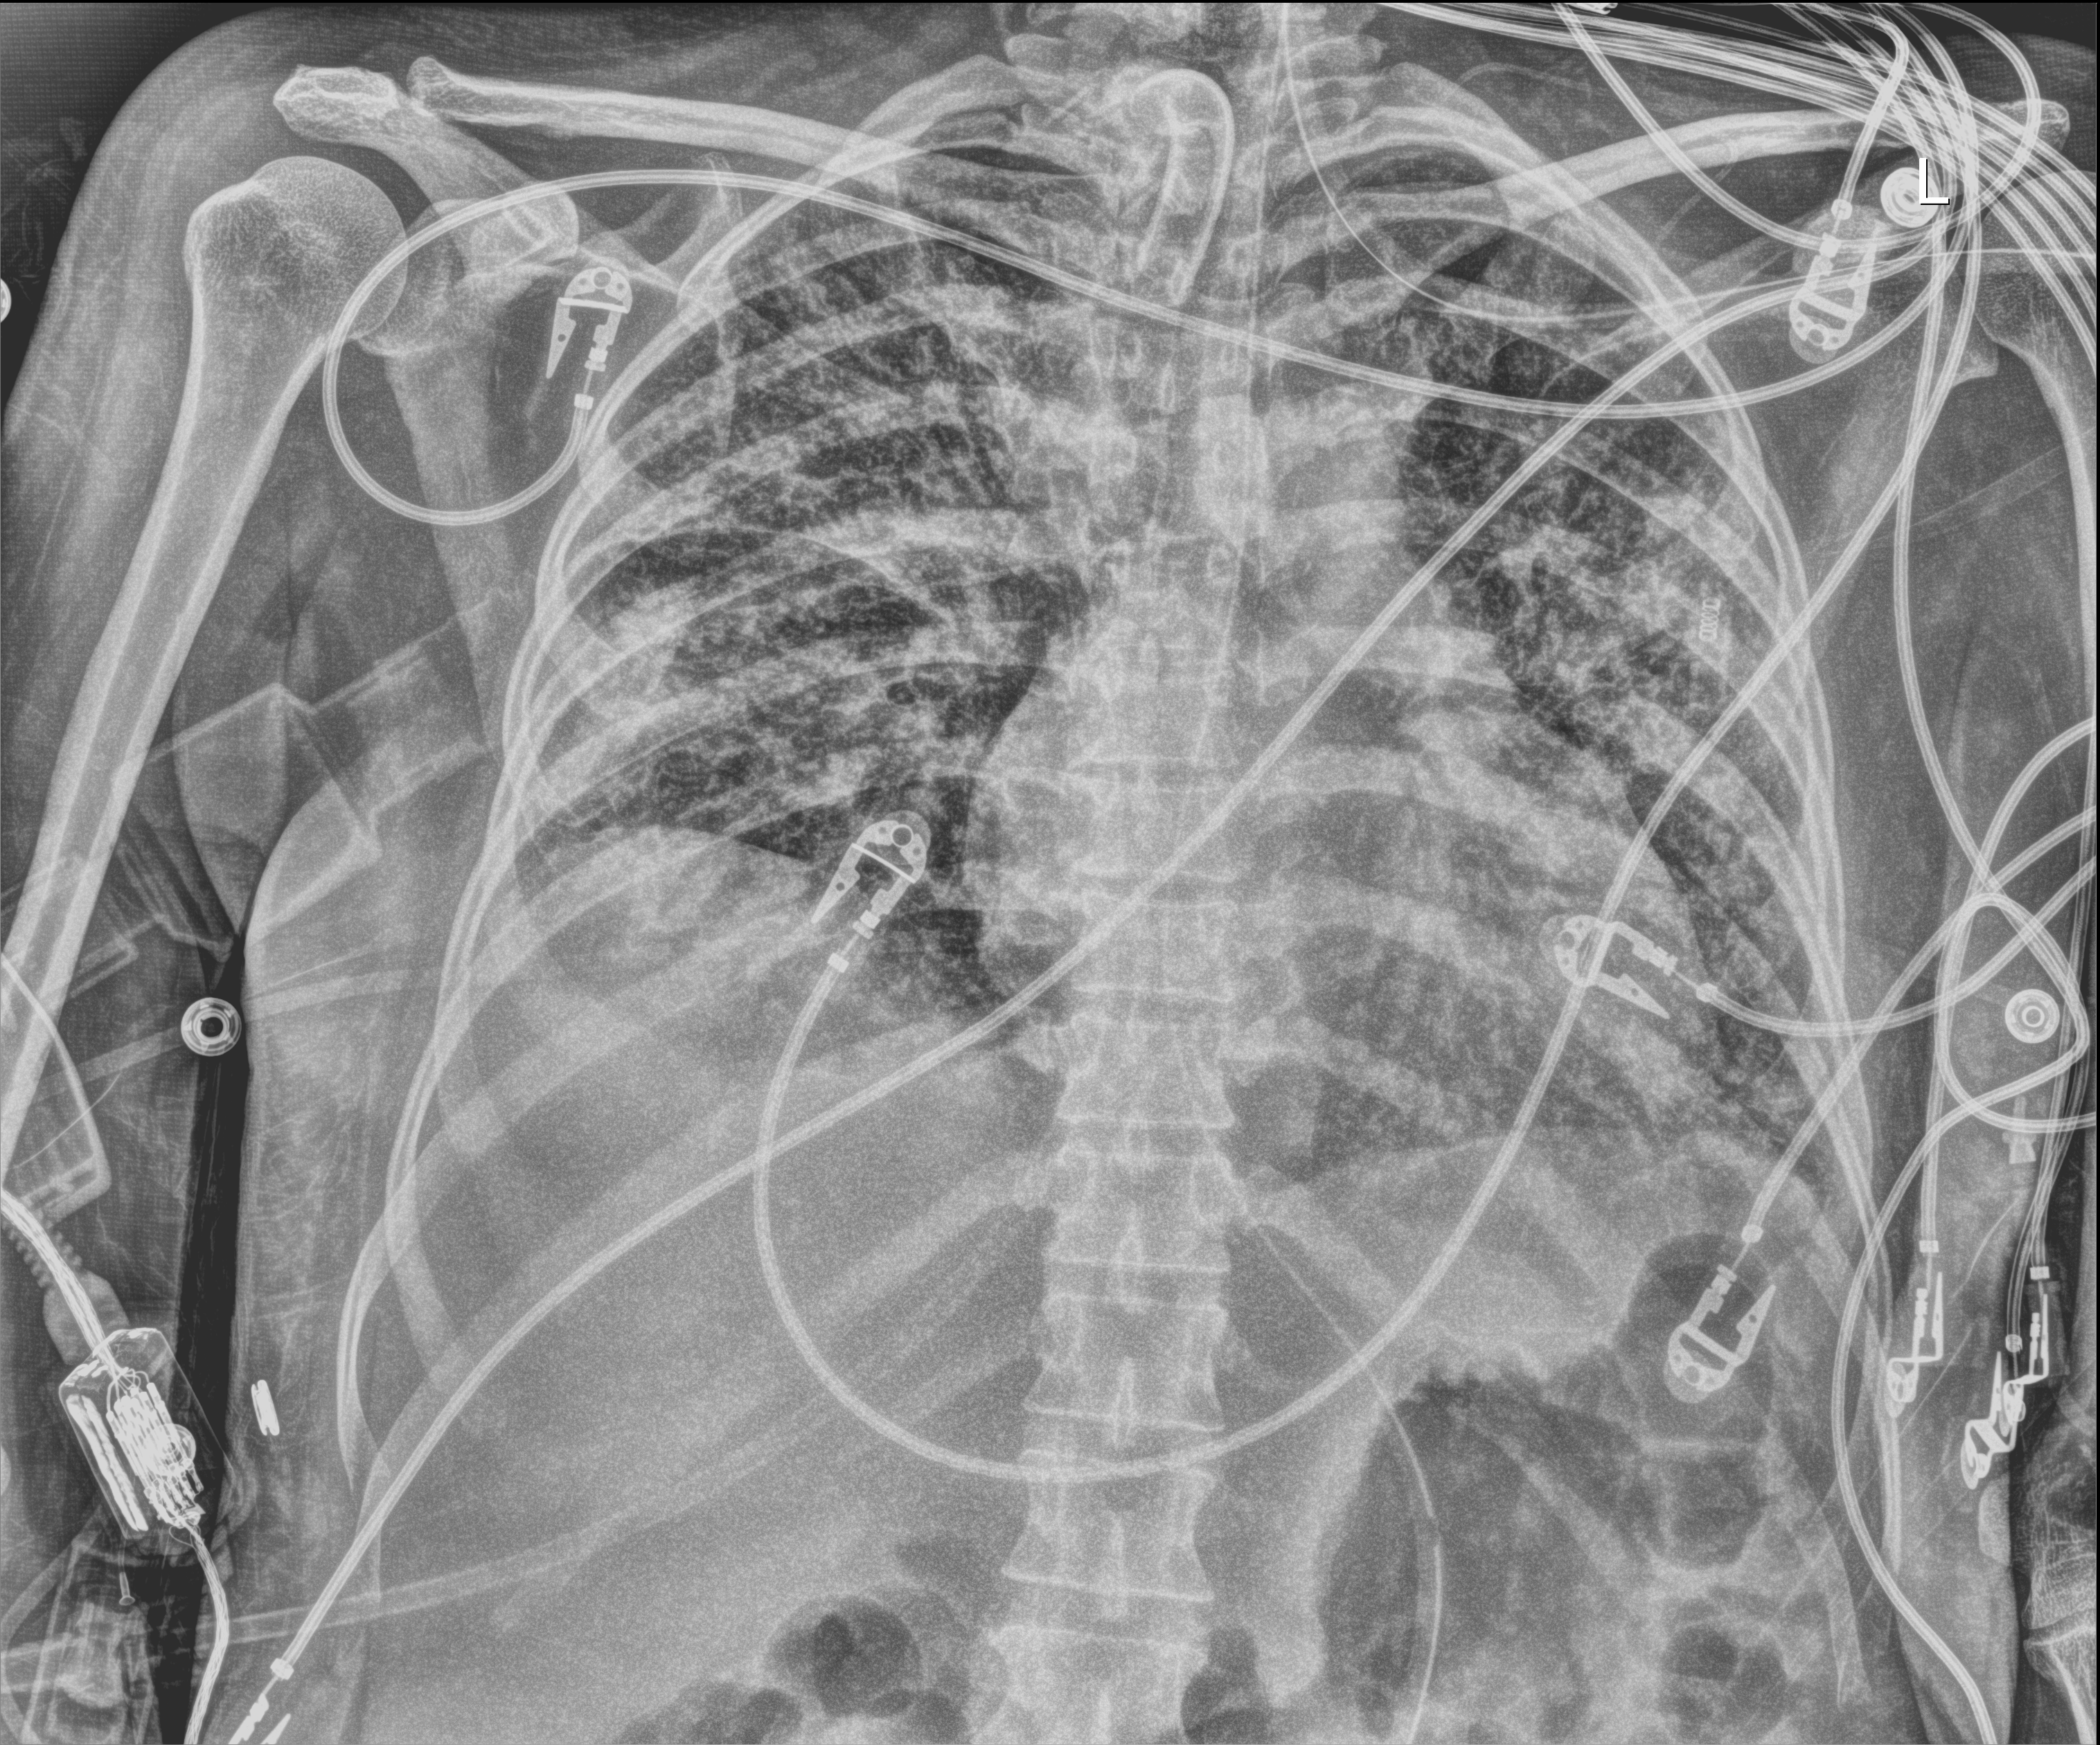
Chest X-ray (portable), anteroposterior (AP) projection. Patient hospitalised with COVID-19; female, aged 18–59 years.
Hospital-stay facts (about this admission, not read from this image; timing relative to this image not recorded):
- mechanically ventilated during this hospital stay: yes